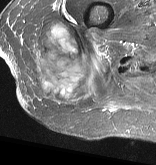
MRI of an extremity soft-tissue mass, one axial slice. Slice 17 of 57 in the series (ordered by position). STIR. MR volume resampled by the dataset authors to the PET/CT grid (not the native acquisition matrix). 3.27 mm slice thickness. 156 × 165 image matrix. Female patient. Case-level facts recorded for this patient, not image findings: histological type: epithelioid sarcoma with vascular differentiation; site of the primary tumour: right buttock.
Outlined on this slice (expert contour drawn on MRI and transferred to this co-registered scan by the dataset authors):
- gross tumour volume (mass): bounding box [x1, y1, x2, y2] px = [31, 21, 109, 106]